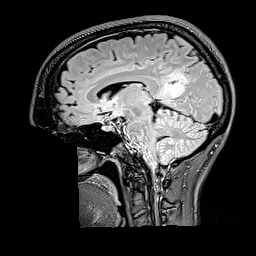
Brain MRI from a brain-tumour surgery series, one sagittal slice; position 93 of 176 along the scan axis; T2 FLAIR; 1 mm slice thickness; 256 × 256 image matrix, field of view 256 × 256 mm. Case-level facts recorded for this patient, not image findings: histopathology: Oligodendroglioma; WHO grade: 2; IDH mutation: yes.
Annotated regions visible in this slice (manually delineated by an expert):
- tumour: box from (x=159, y=69) to (x=189, y=103) px